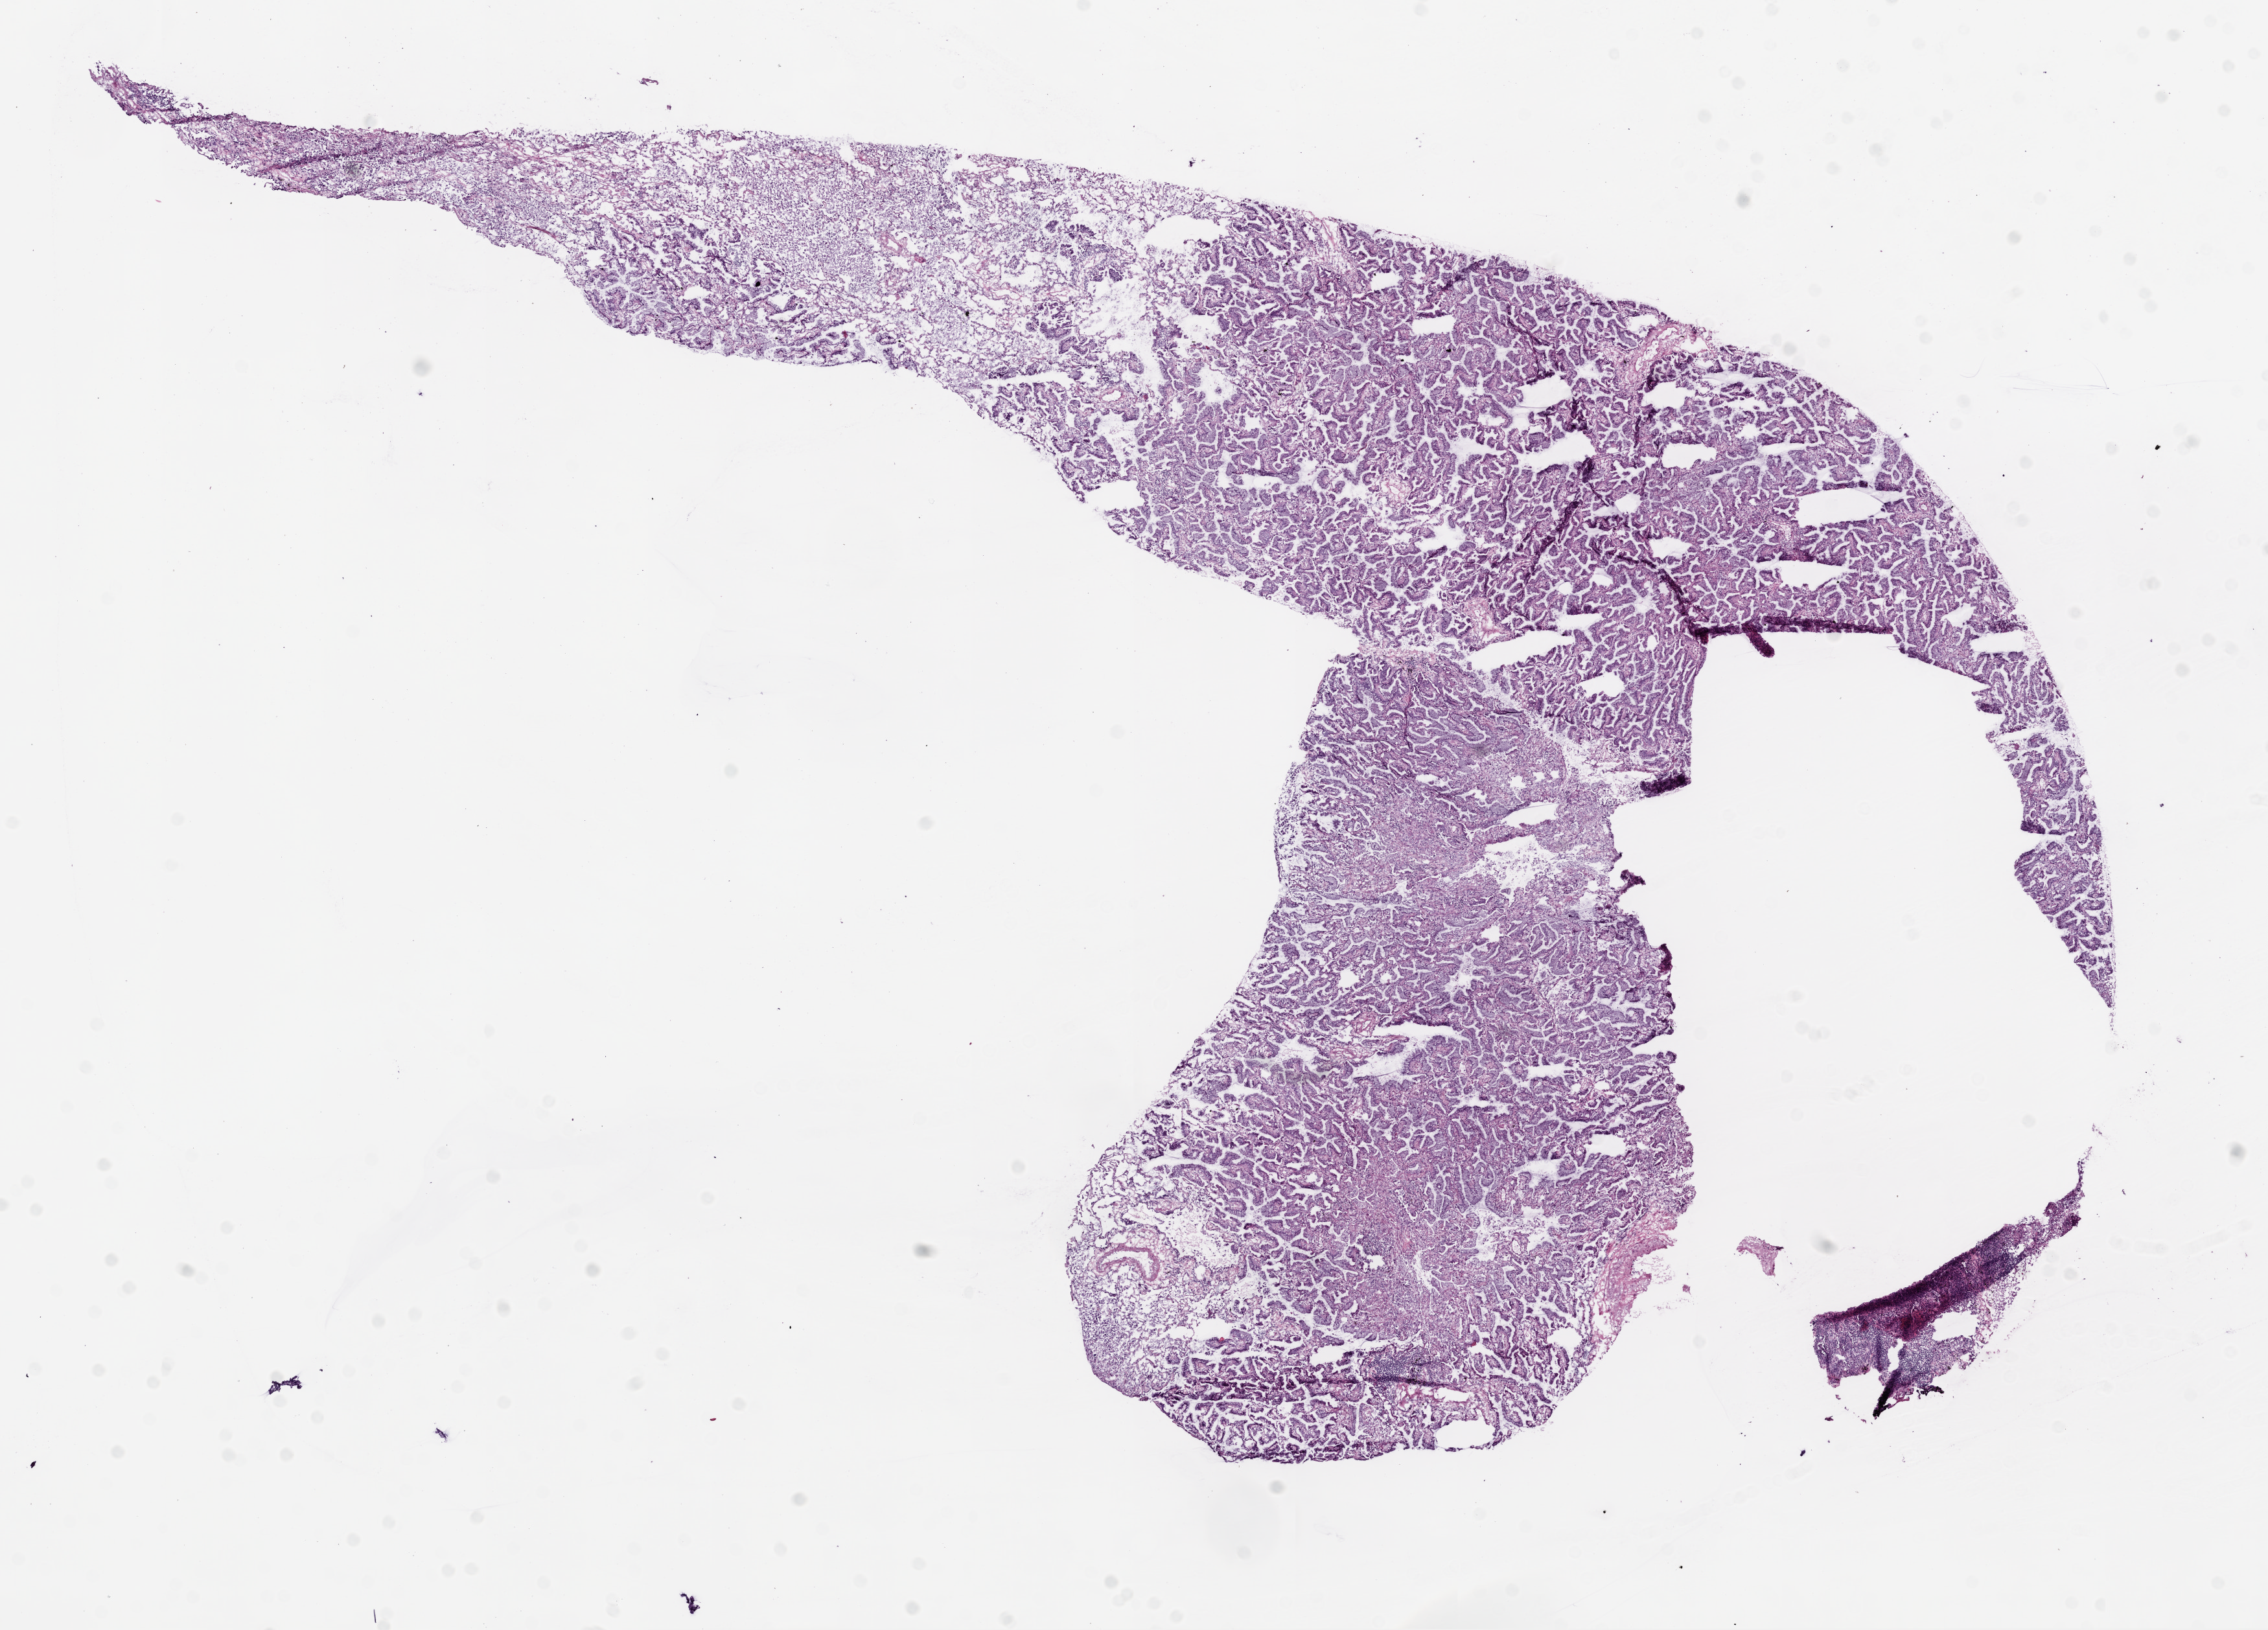
Whole-slide histology image, H&E-stained — low-resolution overview of the scanned area, about 14.0 x 10.1 mm. Frozen section from the bottom of the tissue portion. Lung, primary tumour sample. Male patient; age at initial diagnosis 76 years.
Diagnosis: Adenocarcinoma with mixed subtypes (upper lobe, lung).